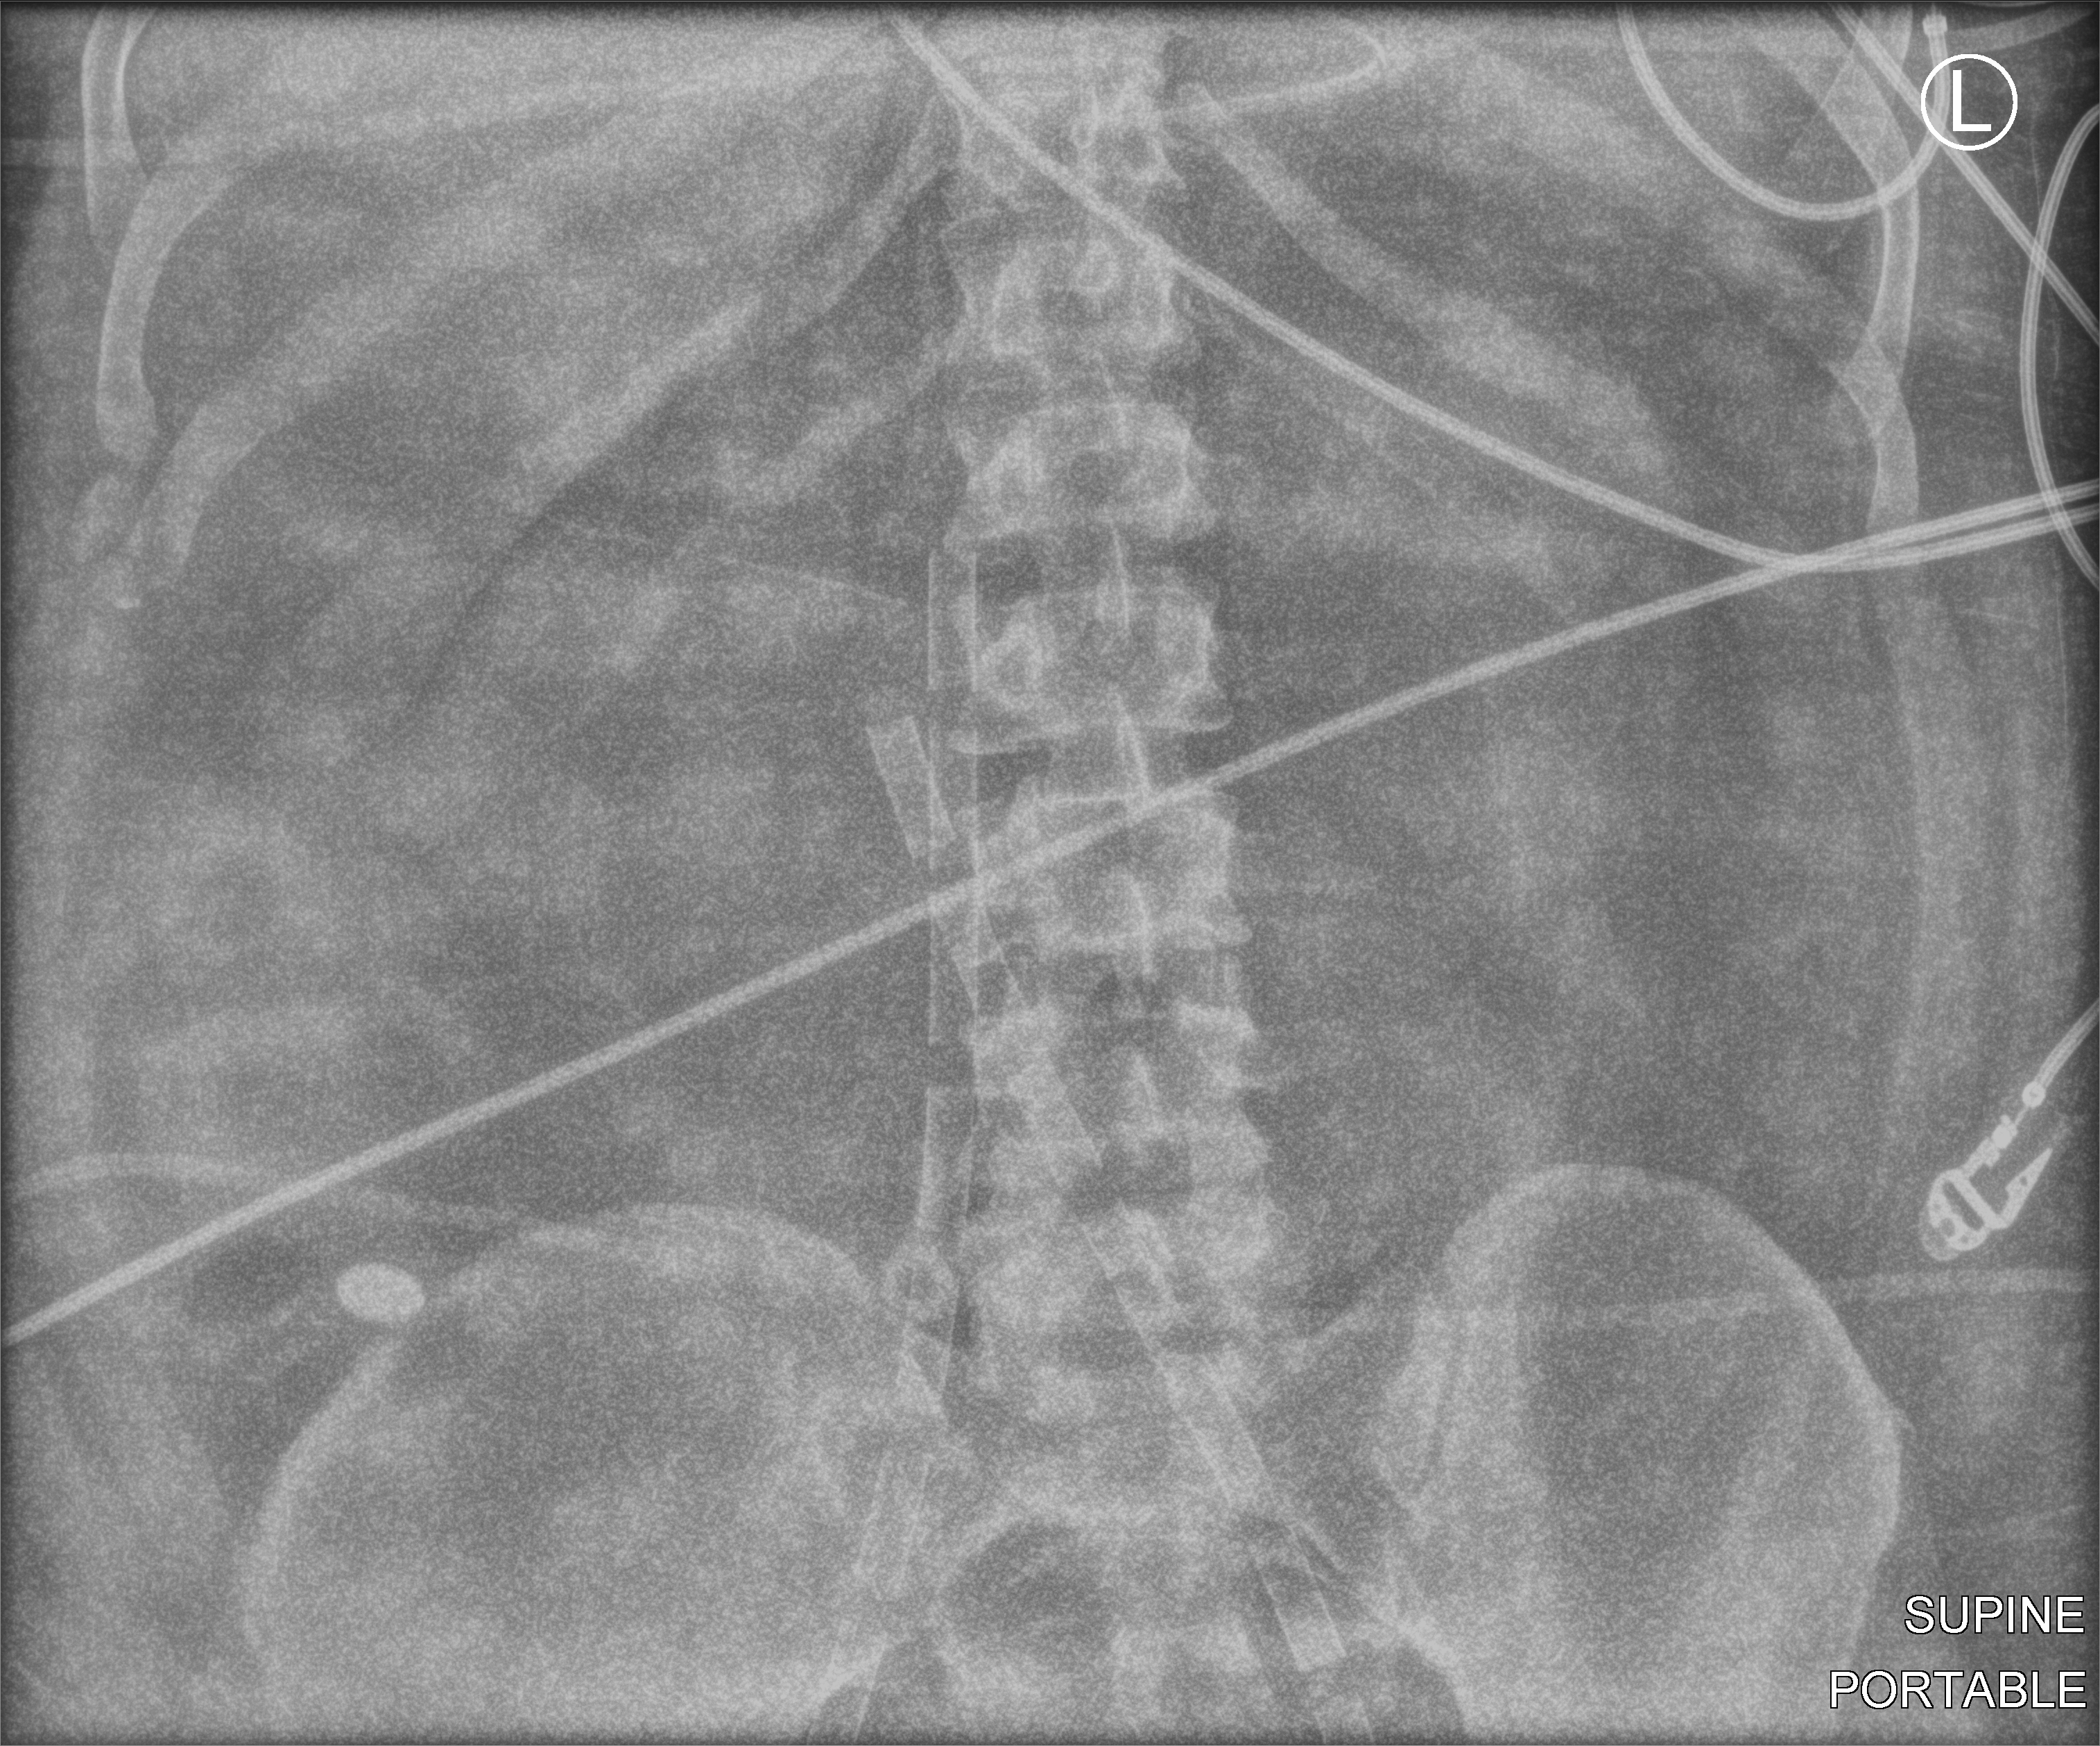
Abdomen X-ray (portable); anteroposterior (AP) projection. Adult patient hospitalised with COVID-19, age 18–59 years.
Hospital-stay facts (about this admission, not read from this image; timing relative to this image not recorded):
- admitted to intensive care during this hospital stay: yes